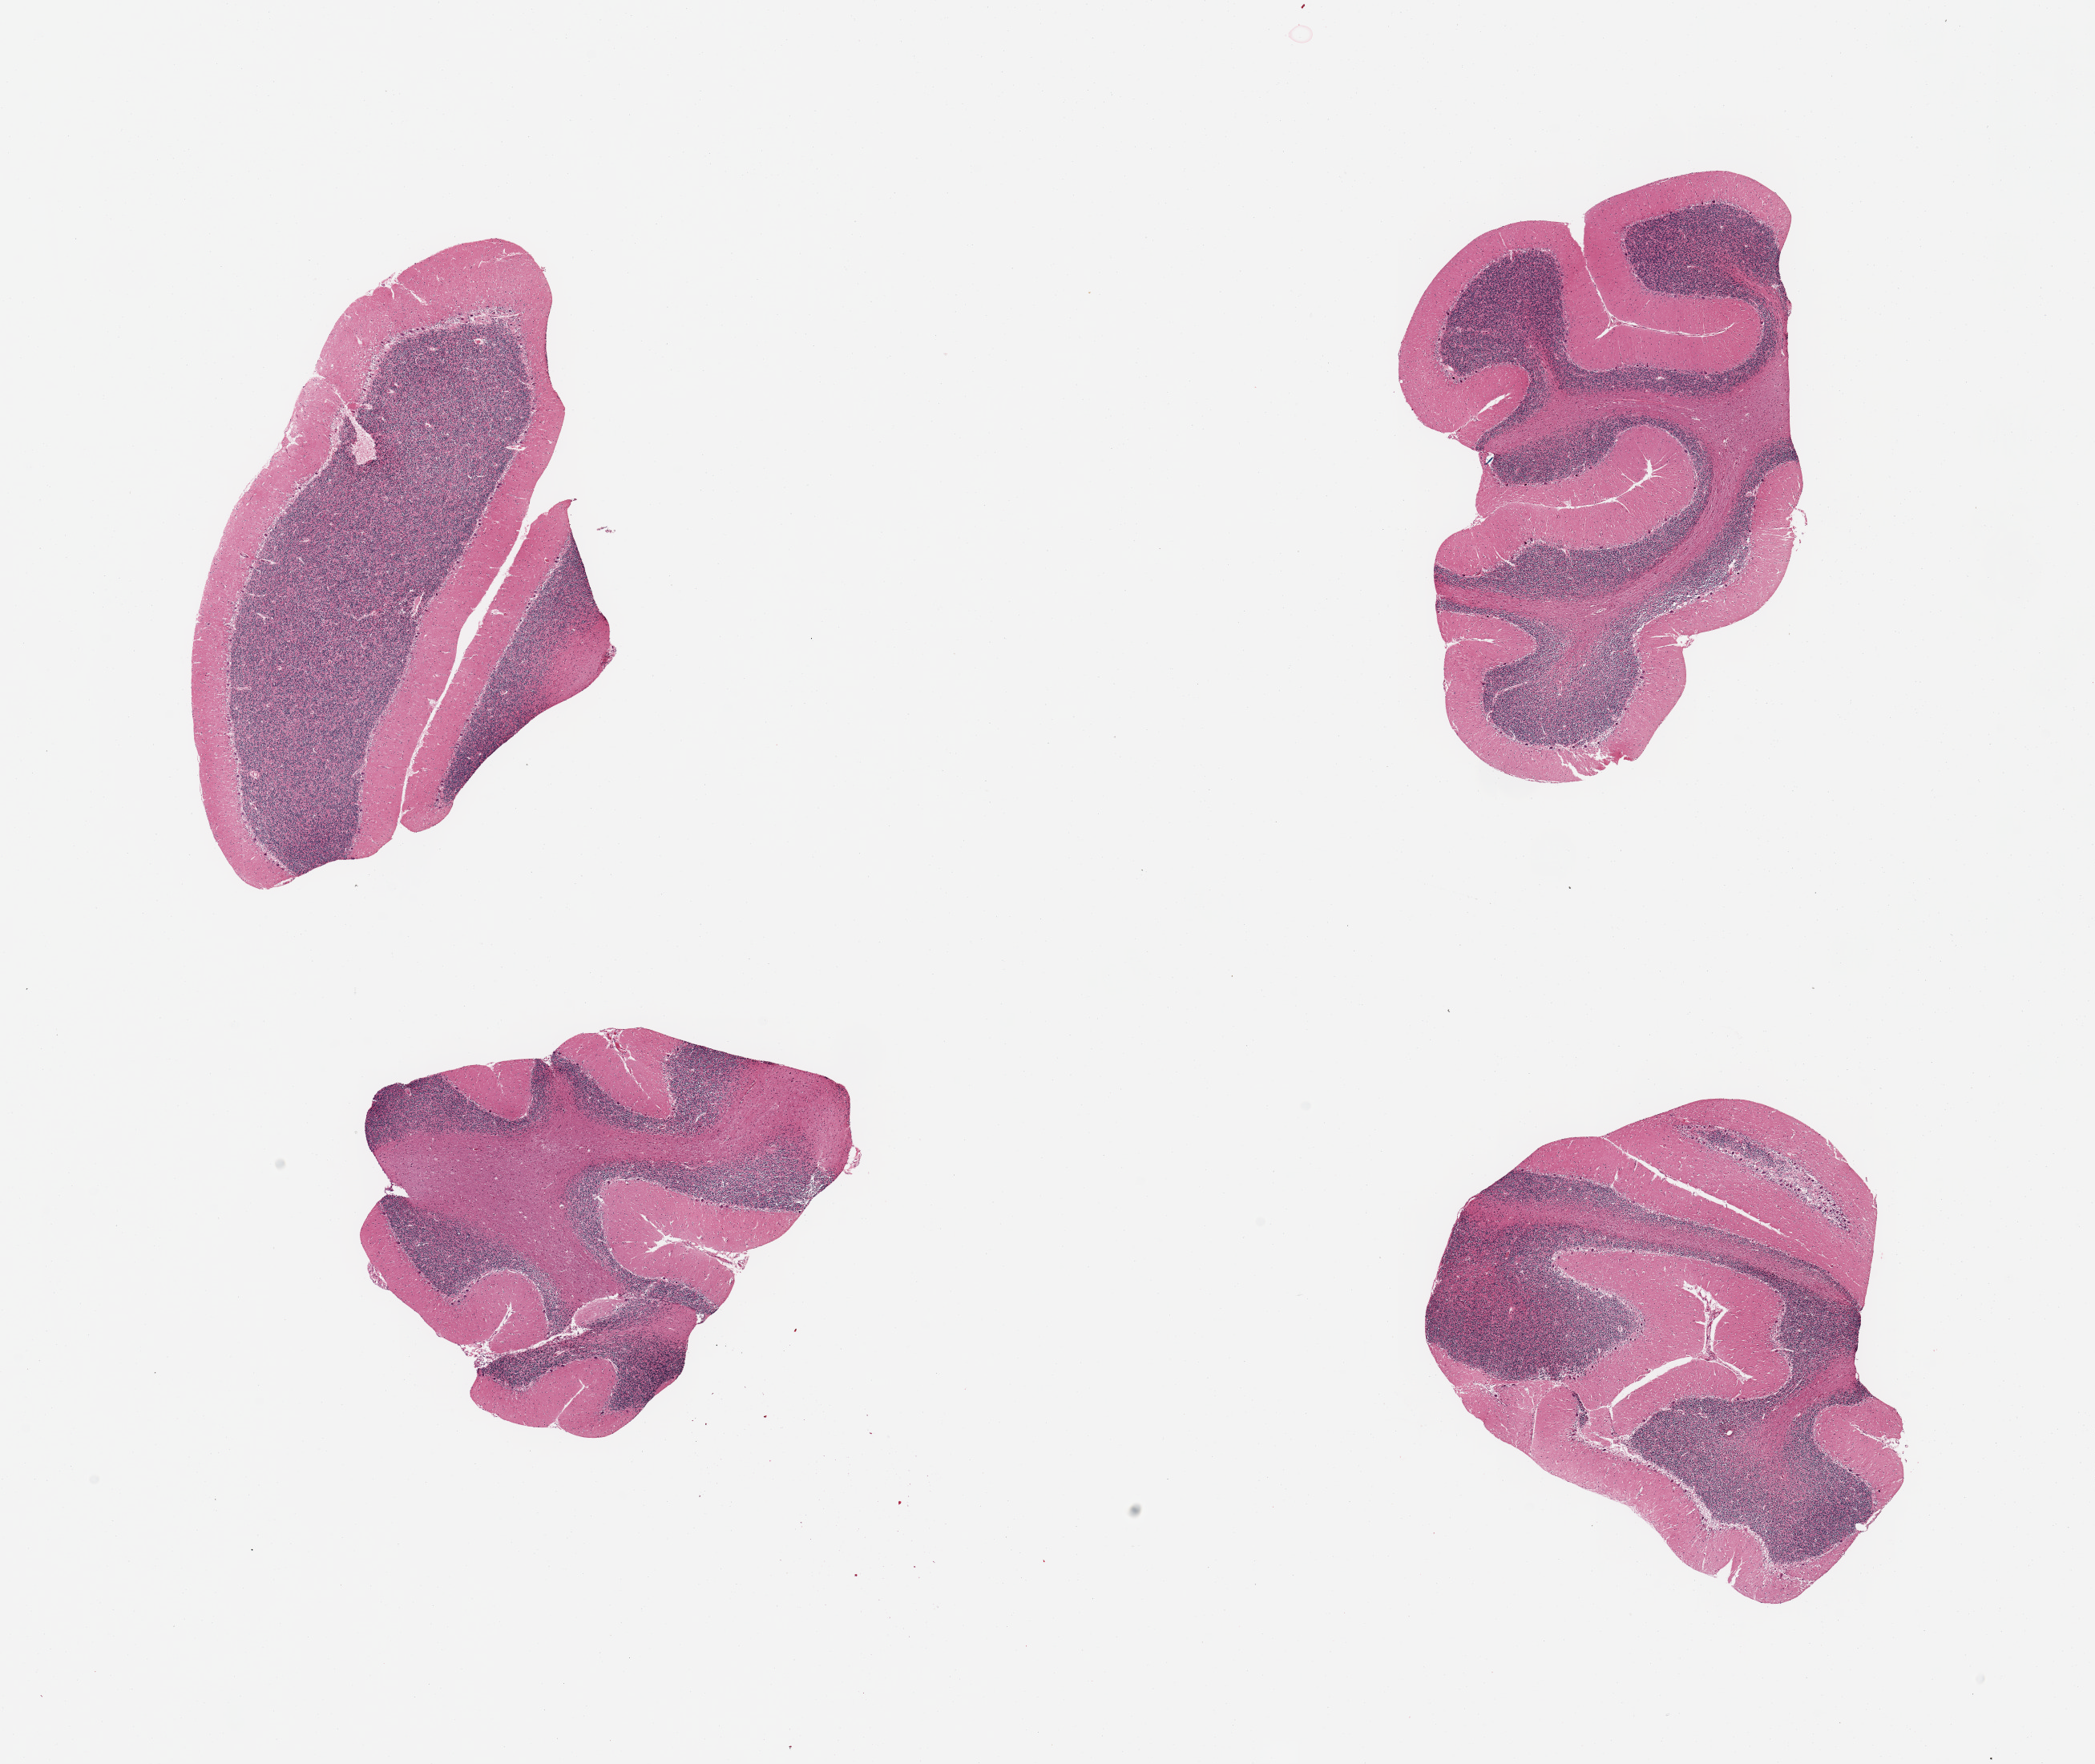
H&E whole-slide image, low-resolution overview of the scanned area, about 20.7 x 17.4 mm. PAXgene-fixed, paraffin-embedded tissue. Target tissue: cerebellum. Donor tissue sample. Female donor.
Review note (as recorded): 4 pieces; purkinje cells well visualized, few with ? evidence of hypoxic damage.